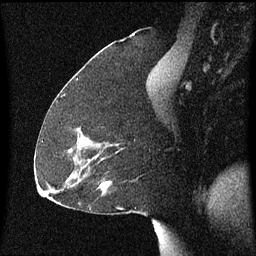
Breast MRI (dynamic contrast-enhanced), one sagittal slice; slice 31 of 60 in the series (ordered by position); dynamic contrast-enhanced series, image 2 of 3 at this slice position (ordered by acquisition); 1.5 T; TE 4.2 ms, TR 8.4 ms; 256 × 256 image matrix, field of view 200 × 200 mm. Patient: female, 59 years.
Outlined on this slice (semi-automatically segmented with operator editing):
- analysis volume of interest (the breast-tissue region the enhancement analysis was run in; not a lesion): bounding box <98,182,111,191> (left, top, right, bottom; pixels)
- tumour enhancement mask (voxels above the 70 % enhancement threshold inside the analysis volume of interest): <100,184,107,187>